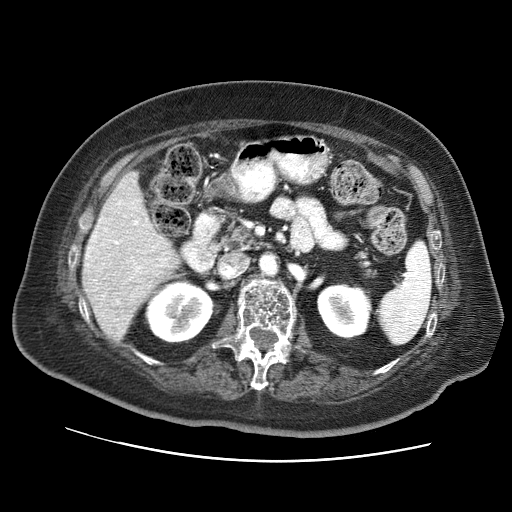
Contrast-enhanced abdominal CT (liver protocol), one axial slice; position 29 of 73 along the scan axis; 120 kVp; soft-tissue window (W 400 / L 40 HU); 512 × 512 image matrix, field of view 380 × 380 mm. From the clinical record (not read from this slice): diagnosis: hepatocellular carcinoma (patient treated with transarterial chemoembolisation; whether this scan precedes or follows treatment is not stated here); TNM stage (as recorded): Stage-I; Child-Pugh class: A; tumour differentiation: well differentiated; tumour nodularity: uninodular.
Annotated regions visible in this slice (semi-automatic segmentation, software-assisted and operator-edited):
- liver parenchyma outside the tumour (the mass and vessels are separate outlines, so this box may not span the whole liver): bounding box (x1, y1, x2, y2) in pixels: (82, 172, 176, 340)
- liver vessels: (86, 201, 168, 303)